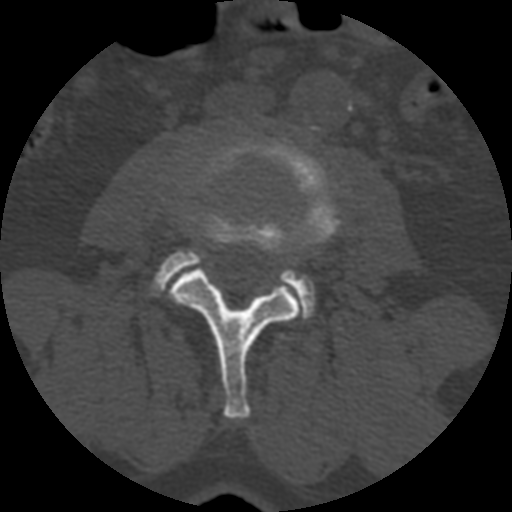
CT including the spine, one axial slice; reconstruction kernel STANDARD; 120 kVp; bone window (W 1800 / L 400 HU); 512 × 512 image matrix, field of view 160 × 160 mm. Patient age 71 years. Case-level facts recorded for this patient, not image findings: primary cancer: prostate.
Outlined on this slice (semi-automatically segmented with operator editing):
- L3 vertebra: box from (x=169, y=137) to (x=341, y=420) px
- L4 vertebra: (x=149, y=249)–(x=315, y=317)